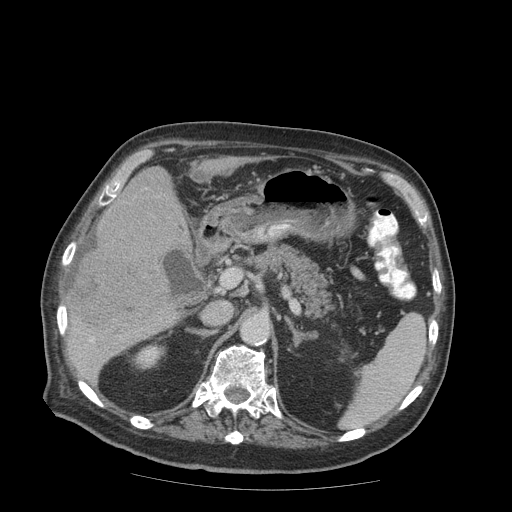
Contrast-enhanced abdominal CT (liver protocol), one axial slice. Position 44 of 99 along the scan axis. 140 kVp. Soft-tissue window (W 400 / L 40 HU). 2.5 mm slice thickness. 512 × 512 image matrix, field of view 420 × 420 mm. Case-level facts recorded for this patient, not image findings: diagnosis: hepatocellular carcinoma (patient treated with transarterial chemoembolisation; whether this scan precedes or follows treatment is not stated here); TNM stage (as recorded): Stage-IIIB; Child-Pugh class: A; tumour differentiation: well differentiated; tumour nodularity: multinodular.
Outlined on this slice (semi-automatic segmentation, software-assisted and operator-edited):
- liver parenchyma outside the tumour (the mass and vessels are separate outlines, so this box may not span the whole liver): box from (x=66, y=166) to (x=190, y=382) px
- mass: (x=67, y=201)–(x=181, y=332)
- liver vessels: (x=90, y=338)–(x=94, y=342)